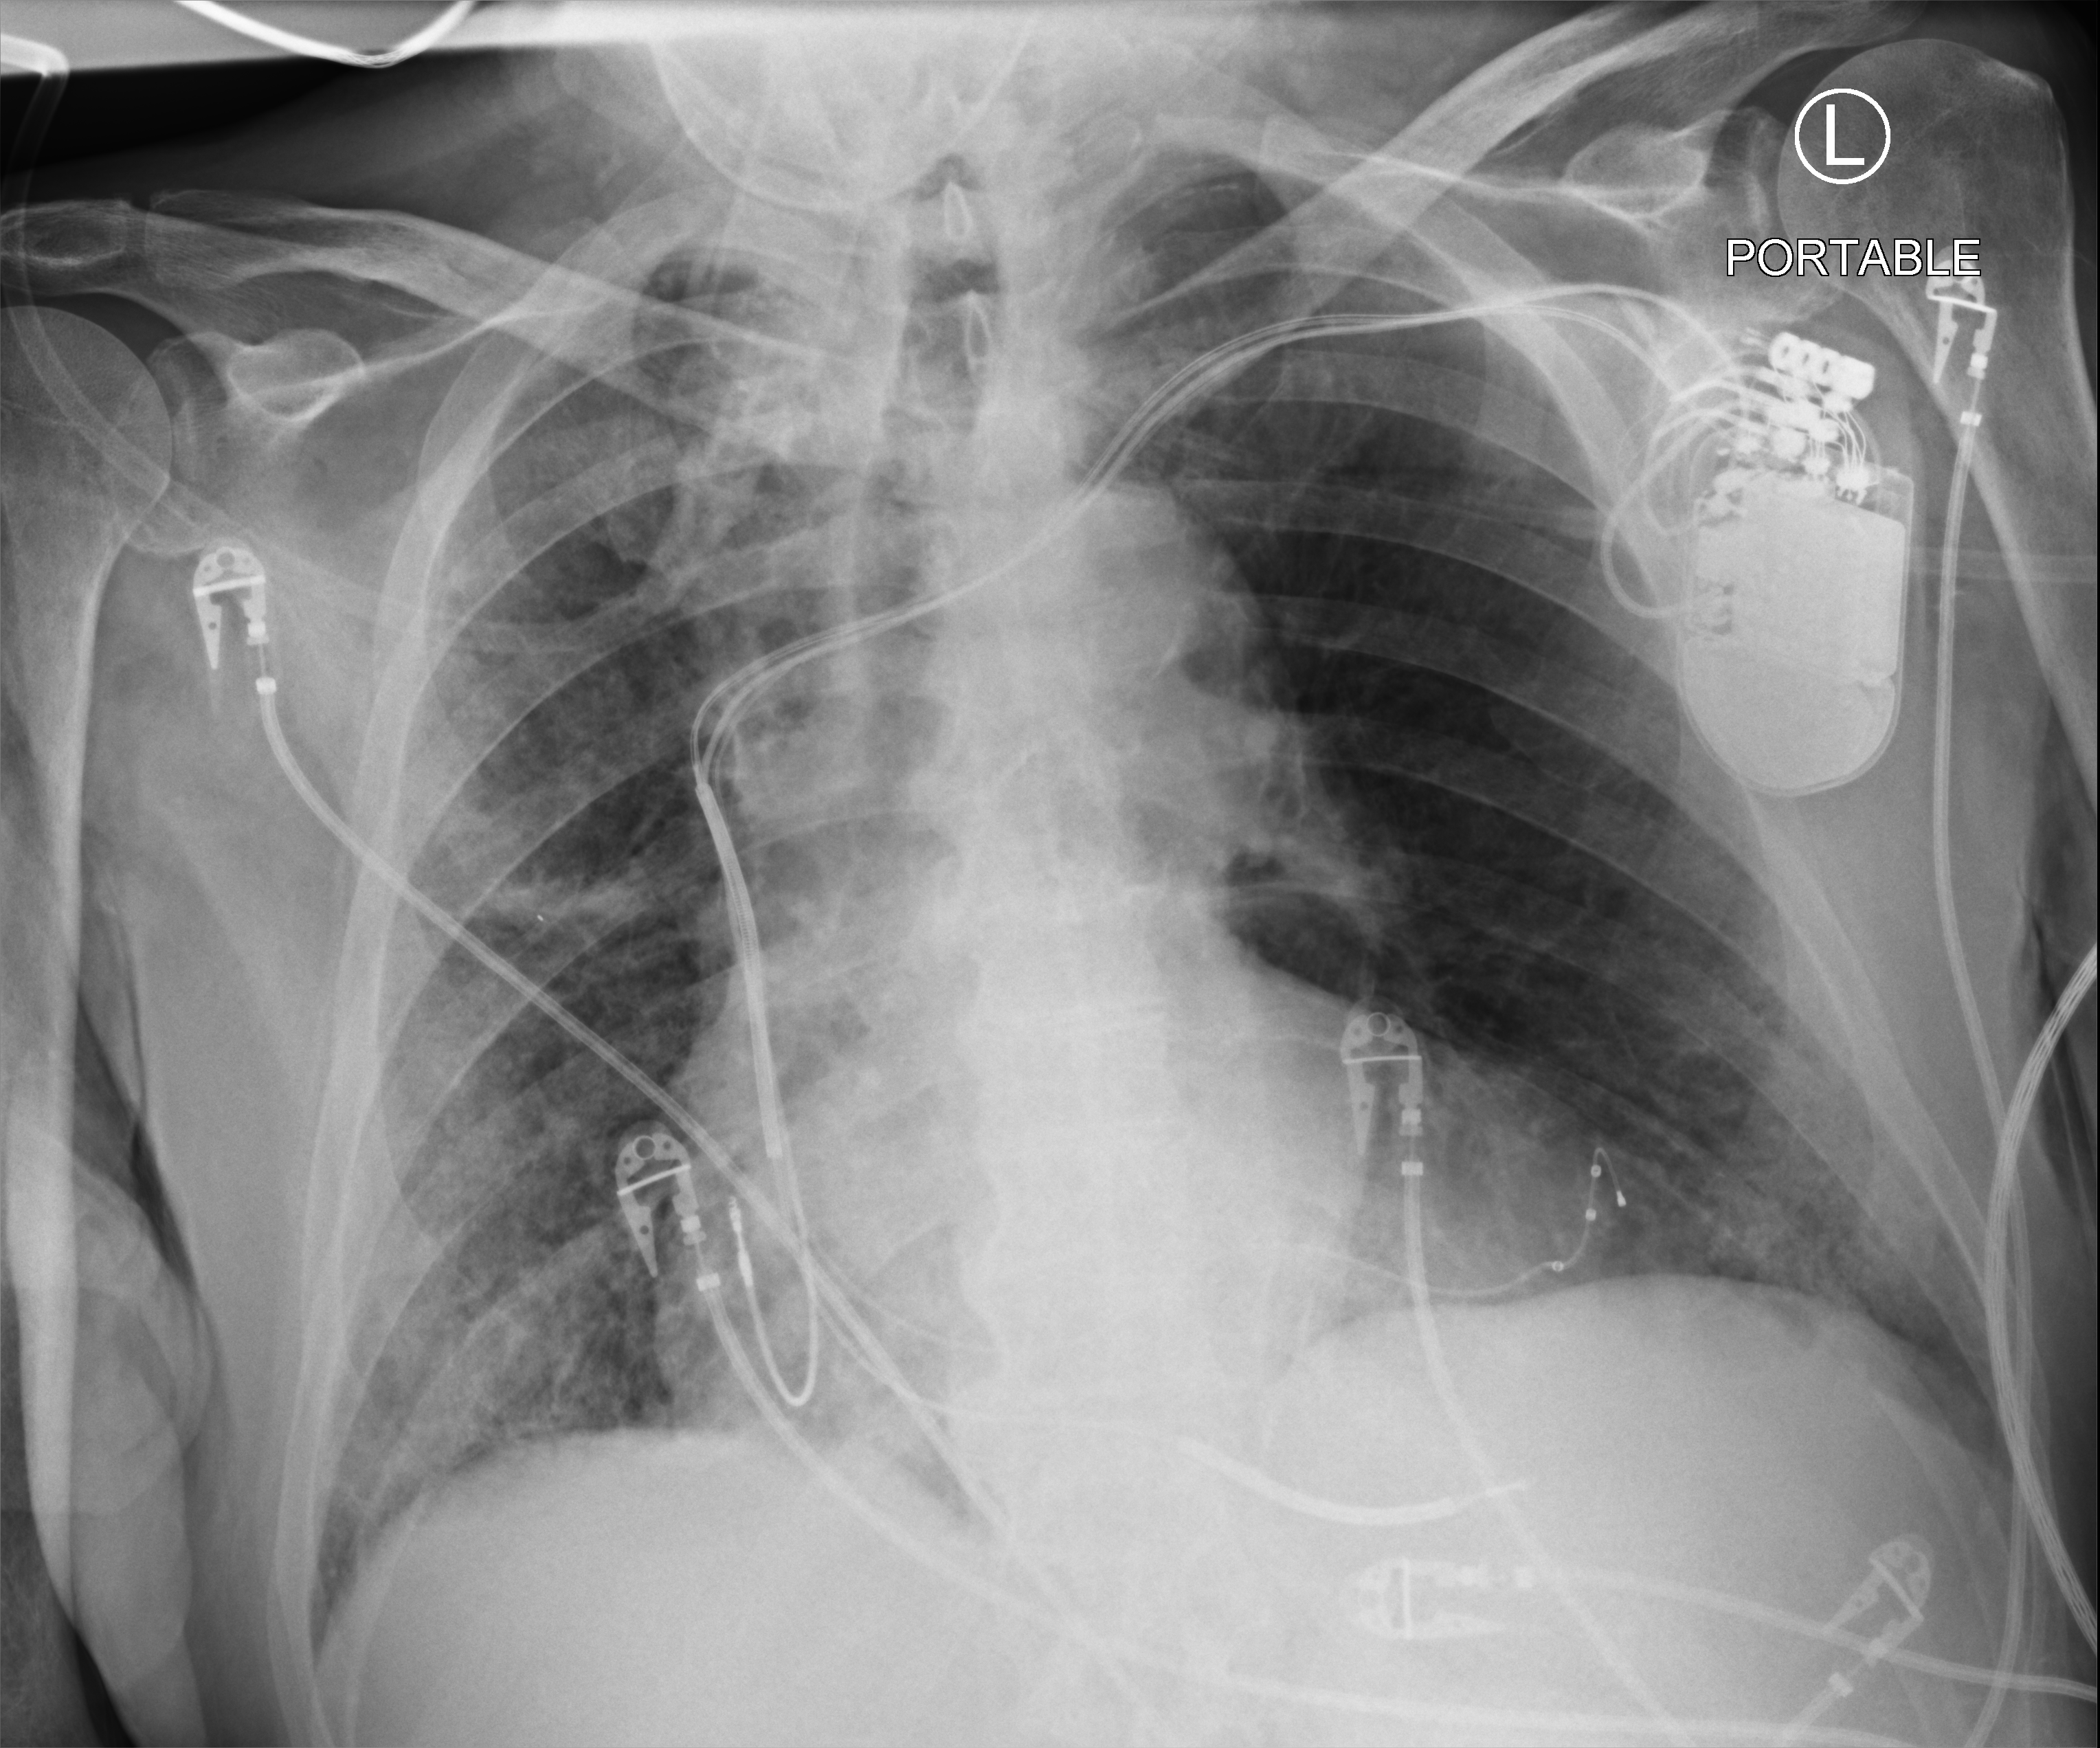
Chest X-ray (portable); anteroposterior (AP) projection. Patient hospitalised with COVID-19; male, aged 75–90 years.
Admission-level facts for this patient (not findings on this image; timing relative to this image not recorded): mechanically ventilated during this hospital stay: no.